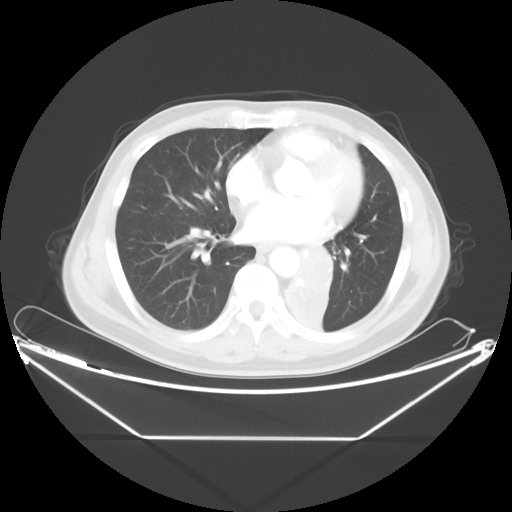
Chest CT, one axial slice; slice 19 of 48 in the series (ordered by position); reconstruction kernel STANDARD; 120 kVp; lung window (W 1500 / L -600 HU); 5 mm slice thickness; 512 × 512 image matrix, field of view 438 × 438 mm. Male patient, age 58 years. From the clinical record (not read from this slice): clinical TNM (as recorded): T3 N3 M0.
Outlined on this slice (bounding box drawn by a radiologist):
- lung tumour (recorded histology: squamous cell carcinoma): box from (x=285, y=242) to (x=338, y=332) px